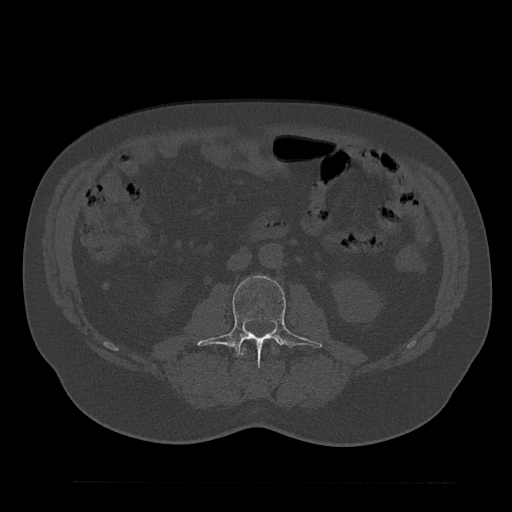
CT including the spine, one axial slice; slice 42 of 797 in the series (ordered by position); reconstruction kernel Br40s/3; bone window (W 1800 / L 400 HU); 512 × 512 image matrix, field of view 430 × 430 mm. Patient: male, 61 years. From the clinical record (not read from this slice): primary cancer: prostate.
Structures marked on this image (semi-automatic segmentation, software-assisted and operator-edited):
- L2 vertebra: box from (x=241, y=346) to (x=275, y=356) px
- L3 vertebra: (x=197, y=275)–(x=323, y=359)